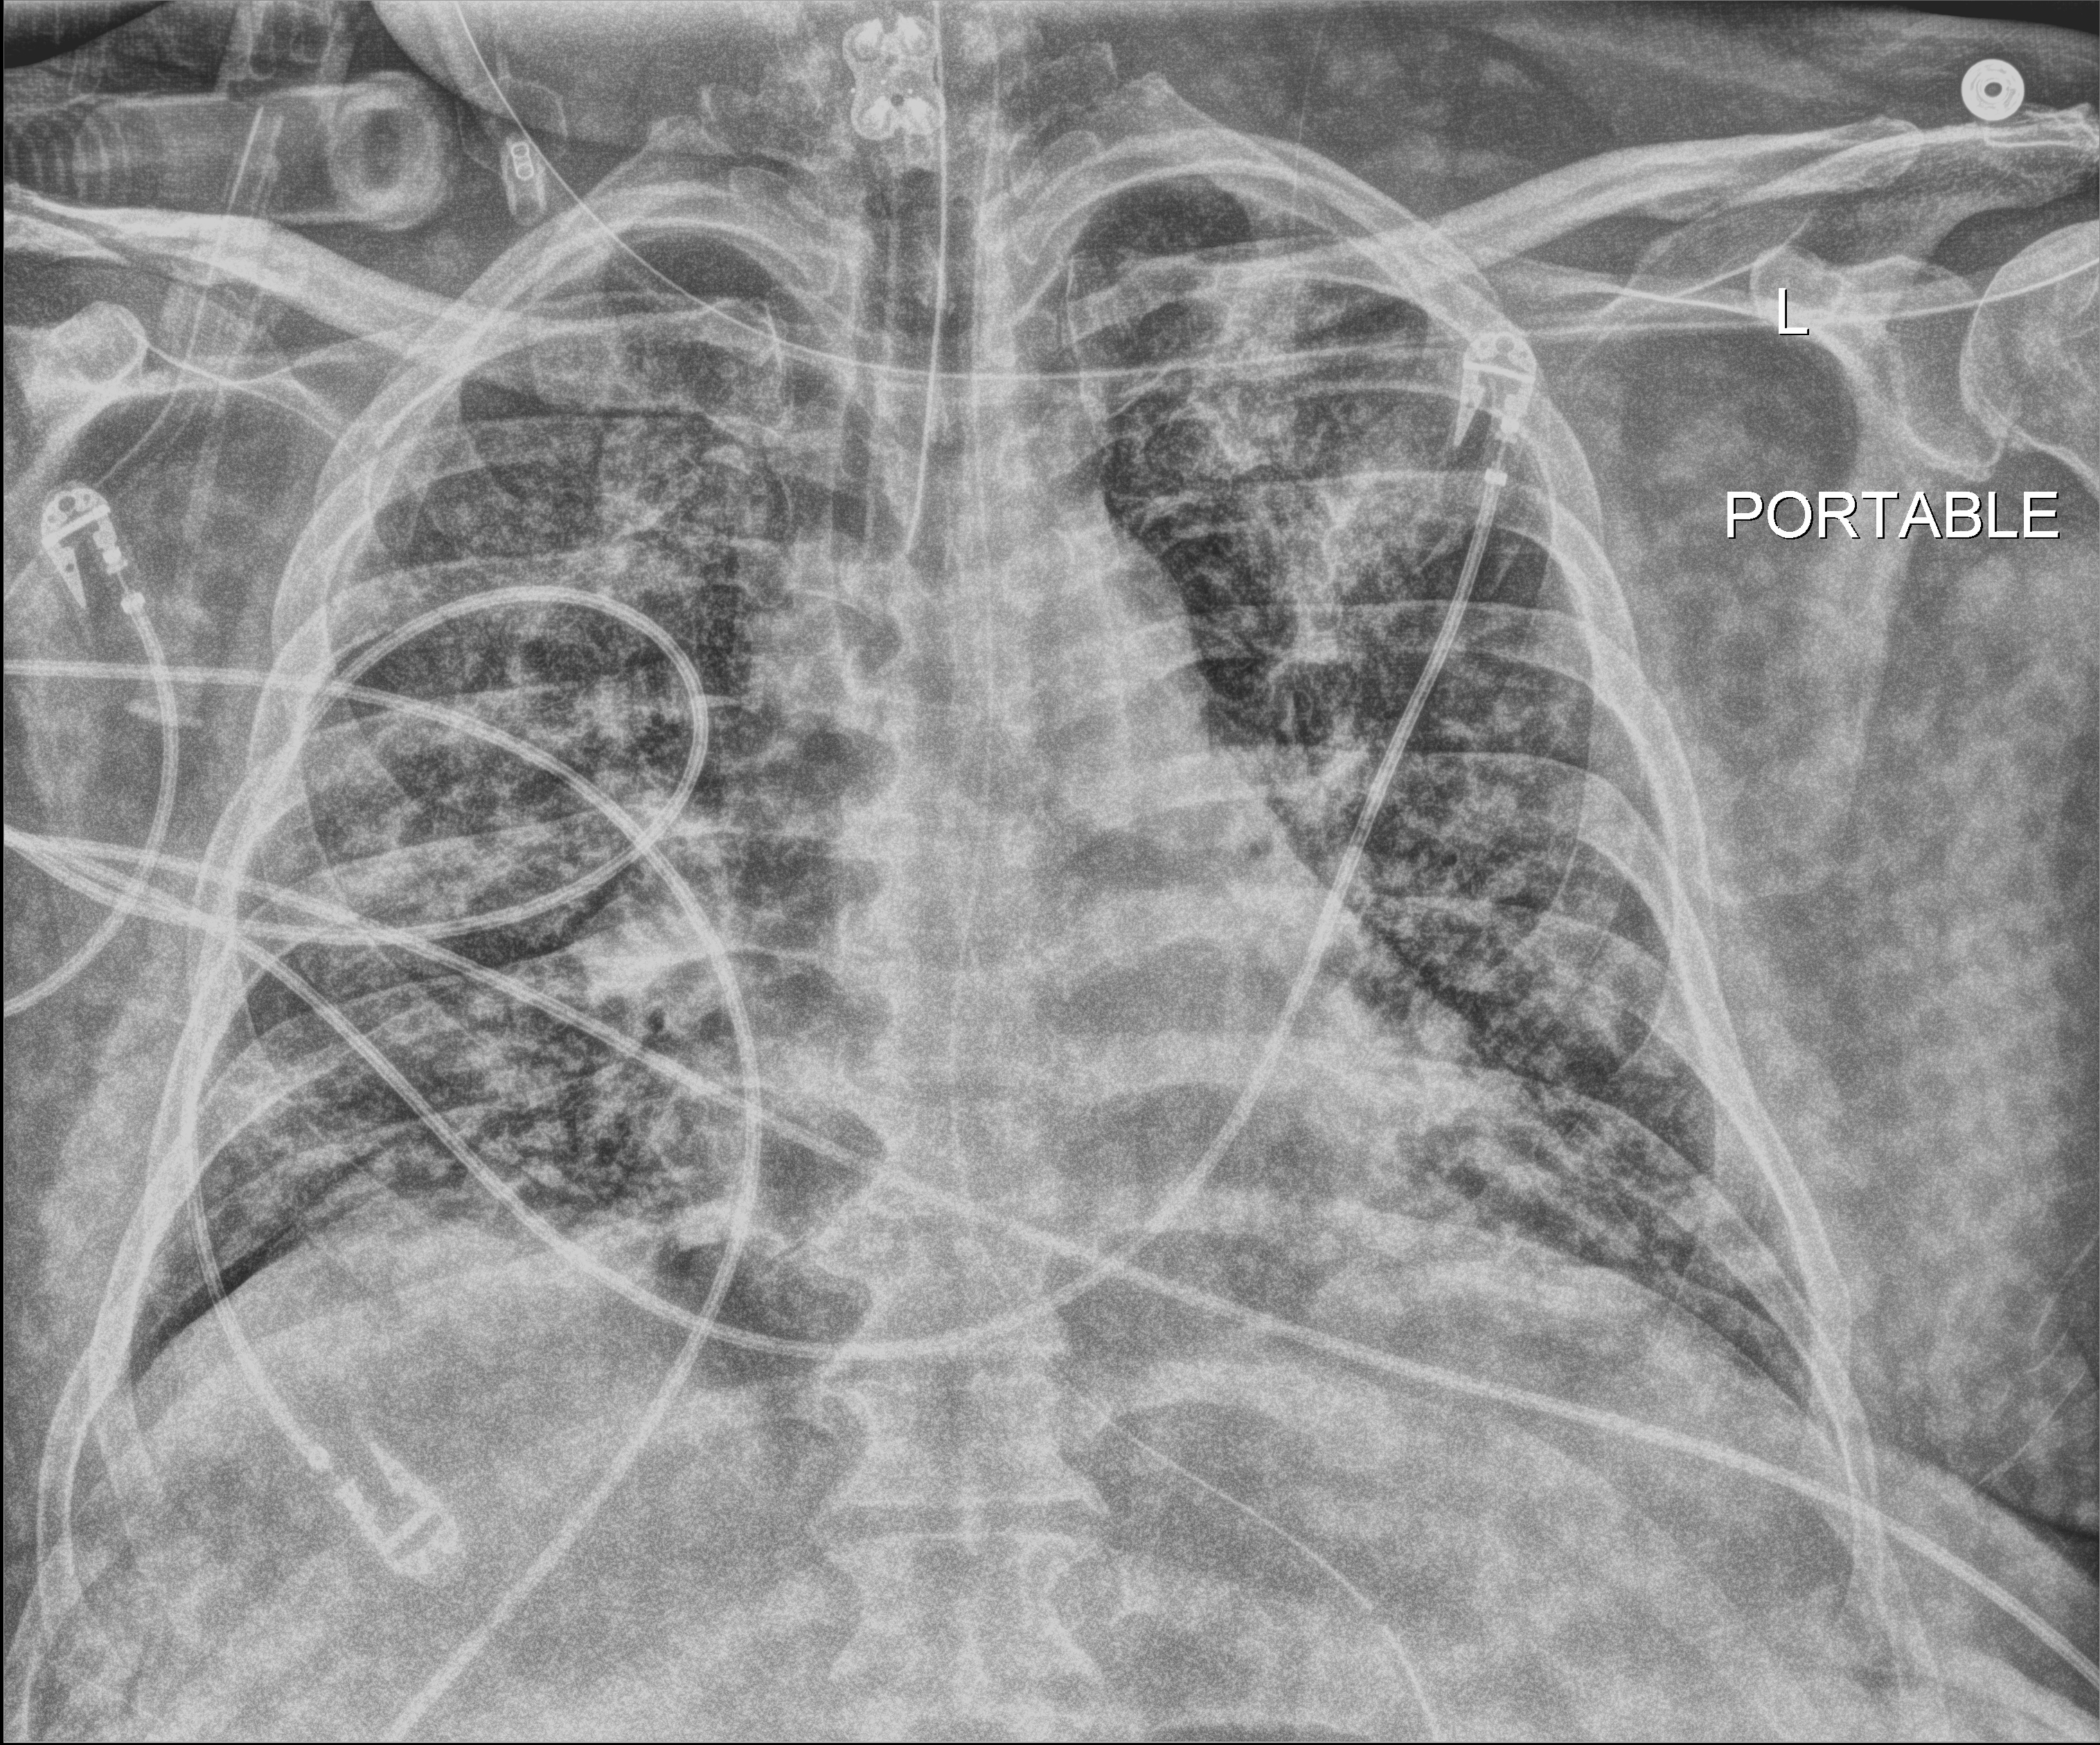
Portable chest radiograph, anteroposterior (AP) projection. Male patient hospitalised with COVID-19, age 18–59 years.
From the hospital-stay record, not from the radiograph (when in the stay this image was taken is not recorded): mechanically ventilated during this hospital stay: yes; COPD (admission record): no; admitted to intensive care during this hospital stay: yes.